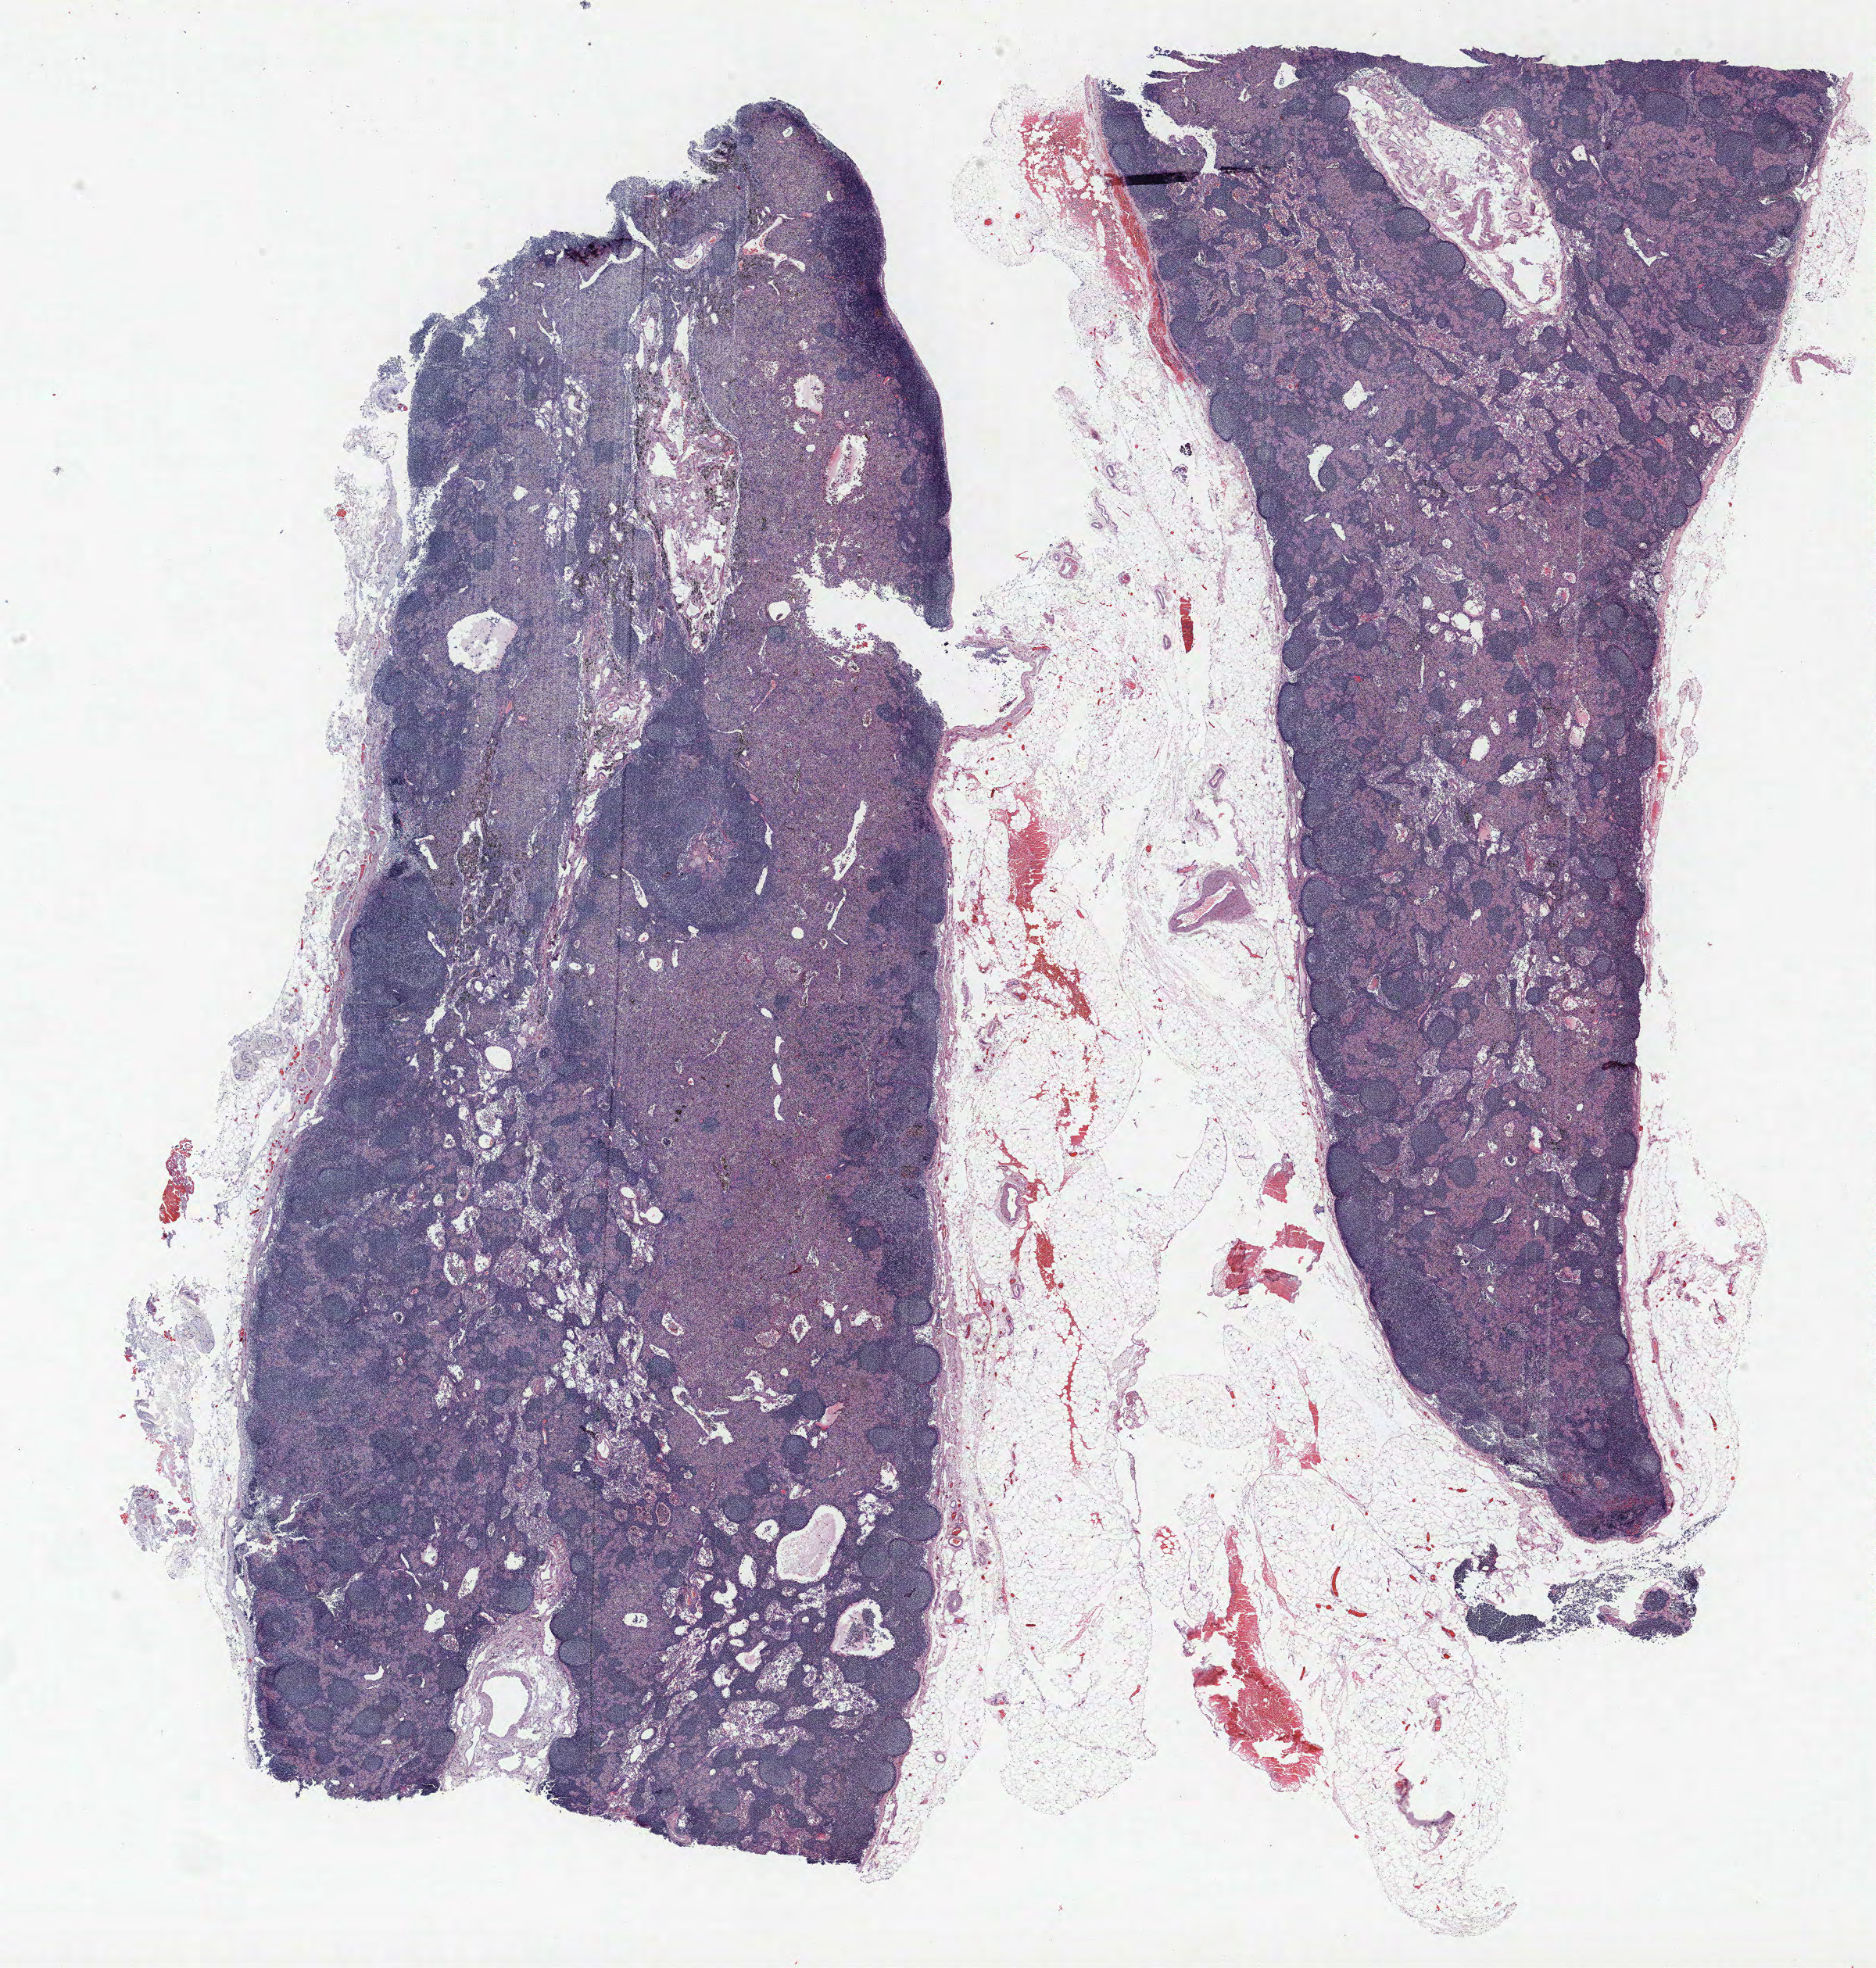
Whole-slide histology image, H&E-stained, a low-resolution overview of the entire scanned area, about 19.2 x 20.1 mm (from a 40x scan). FFPE section. Lung. Male, age 65 at enrolment. Current smoker at enrolment. Grade: poorly differentiated (G3).
• primary tumour location (clinical record): right lower lobe
• tumour size (pathology): 25 mm
• stage (AJCC 6th edition): IIIA
• participant's lung-cancer diagnosis: Adenocarcinoma, NOS